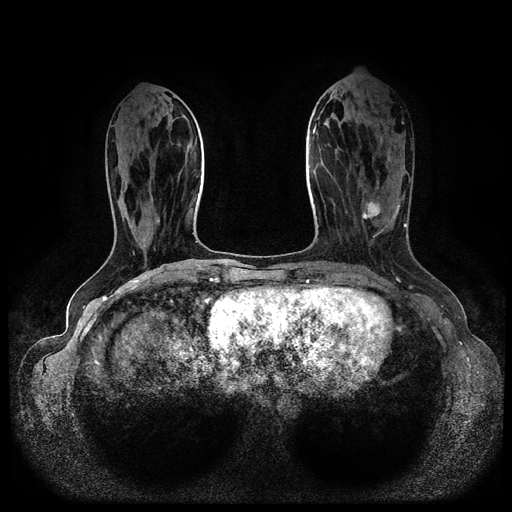
Breast MRI (dynamic contrast-enhanced, multi-phase), one axial slice. Slice 36 of 116 in the series (ordered by position). Dynamic contrast-enhanced series, time point 2 of 5 at this slice position (early post-contrast). 1.5 T. TE 2.6 ms, TR 5.3 ms. 2 mm slice thickness. 512 × 512 image matrix, field of view 350 × 350 mm. Female patient, age 45 years.
Annotated regions visible in this slice (semi-automatically segmented with operator editing):
- breast lesion (labelled 'tumour' in the annotation; benign lesions carry a separate 'benign' label): bounding box [x1, y1, x2, y2] px = [361, 198, 381, 225]